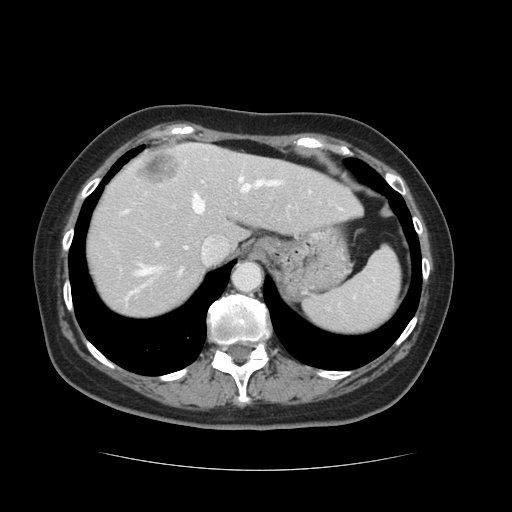
Contrast-enhanced abdominal CT, one axial slice; position 101 of 128 along the scan axis; soft-tissue window (W 400 / L 40 HU); 512 × 512 image matrix. Female patient, age 67 years. Case-level facts recorded for this patient, not image findings: diagnosis: colorectal cancer liver metastases, imaged before liver resection; multiple liver metastases: yes; largest metastasis: 3 cm.
Structures marked on this image (outlined manually by an expert reader):
- hepatic veins: bounding box <127,177,282,299> (left, top, right, bottom; pixels)
- liver: <86,144,359,319>
- planned liver remnant (the part of the liver to remain after resection): <86,153,359,319>
- portal vein (with intrahepatic branches): <157,160,220,245>
- liver metastasis: <137,154,179,183>